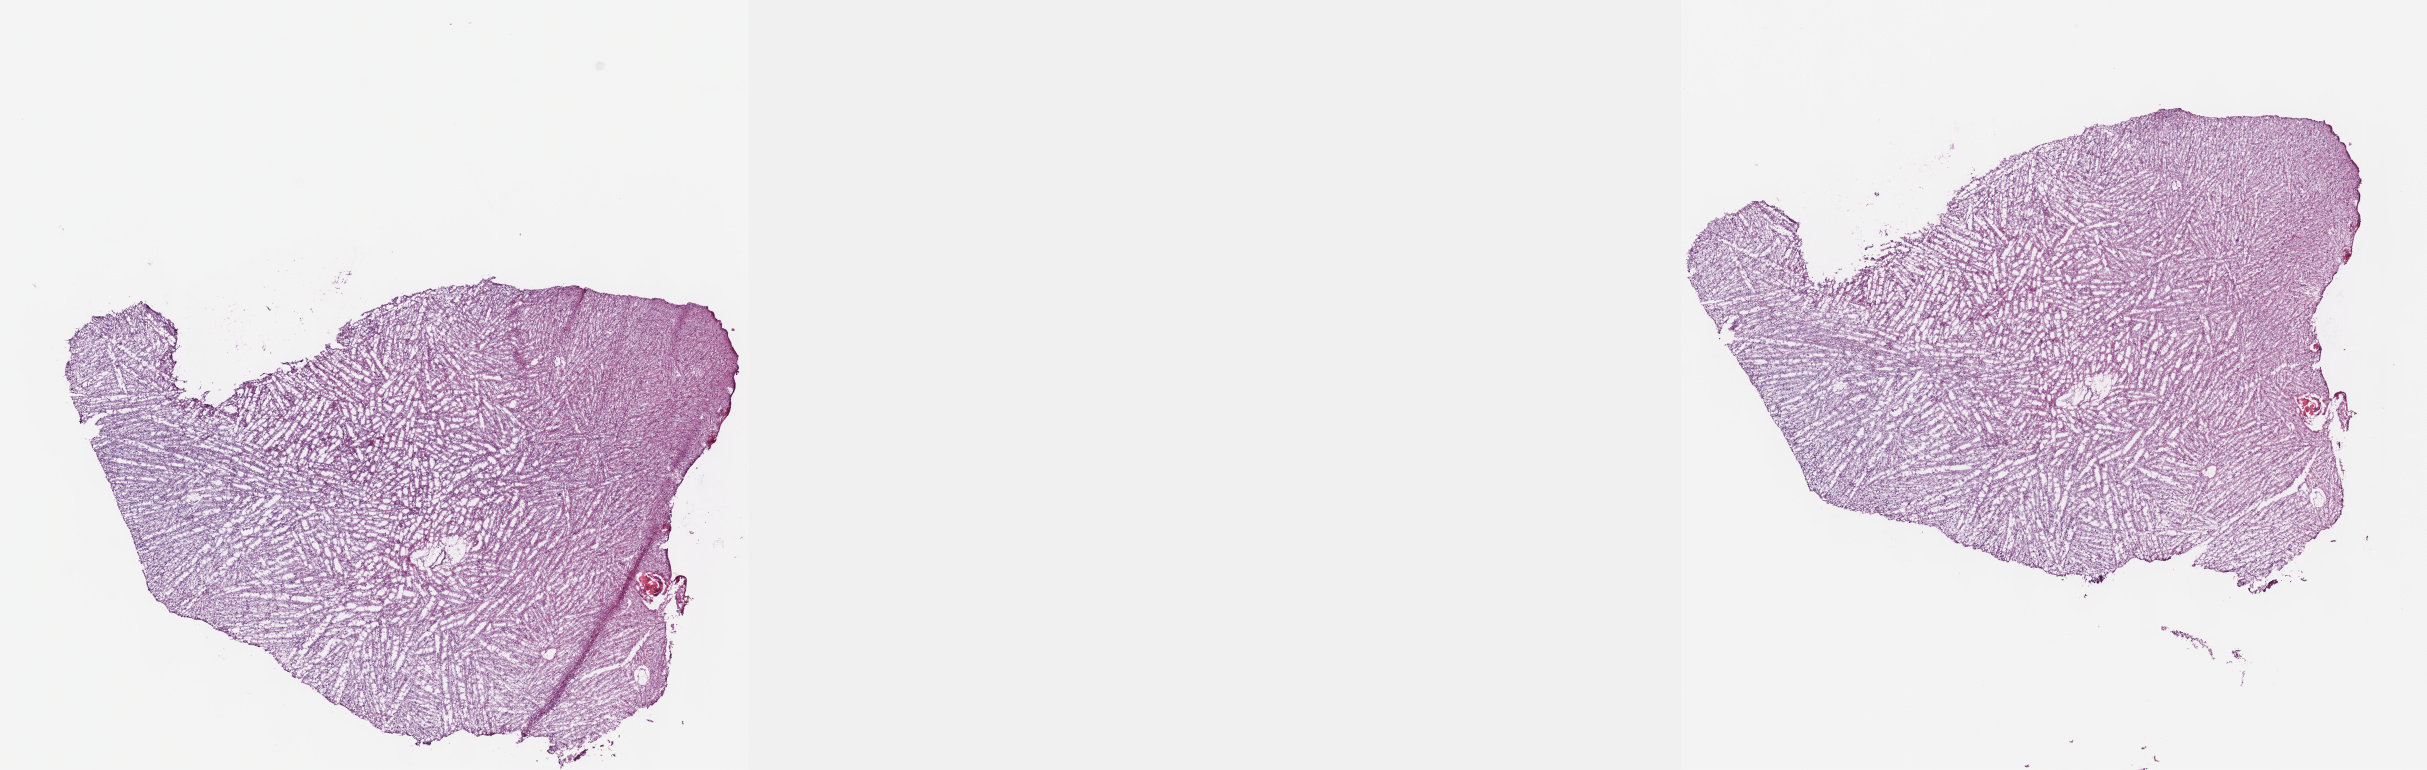
Digitized H&E-stained tissue section (whole slide), low-resolution overview of the scanned area, about 19.6 x 6.2 mm (acquisition: 40x scan); frozen section from the top of the tissue portion; sample: primary tumour, brain. Male patient; age at initial diagnosis 36 years. Histologic grade: G2 (moderately differentiated). Slide review estimates, as recorded: tumour cells 40%, tumour nuclei 80%, normal cells 10%, stromal cells 50%, necrosis 0%. Inflammatory infiltration, as recorded: lymphocyte infiltration 0%, monocyte infiltration 0%, neutrophil infiltration 0%.
Laterality: left. Pathologic diagnosis: Mixed glioma (cerebrum).